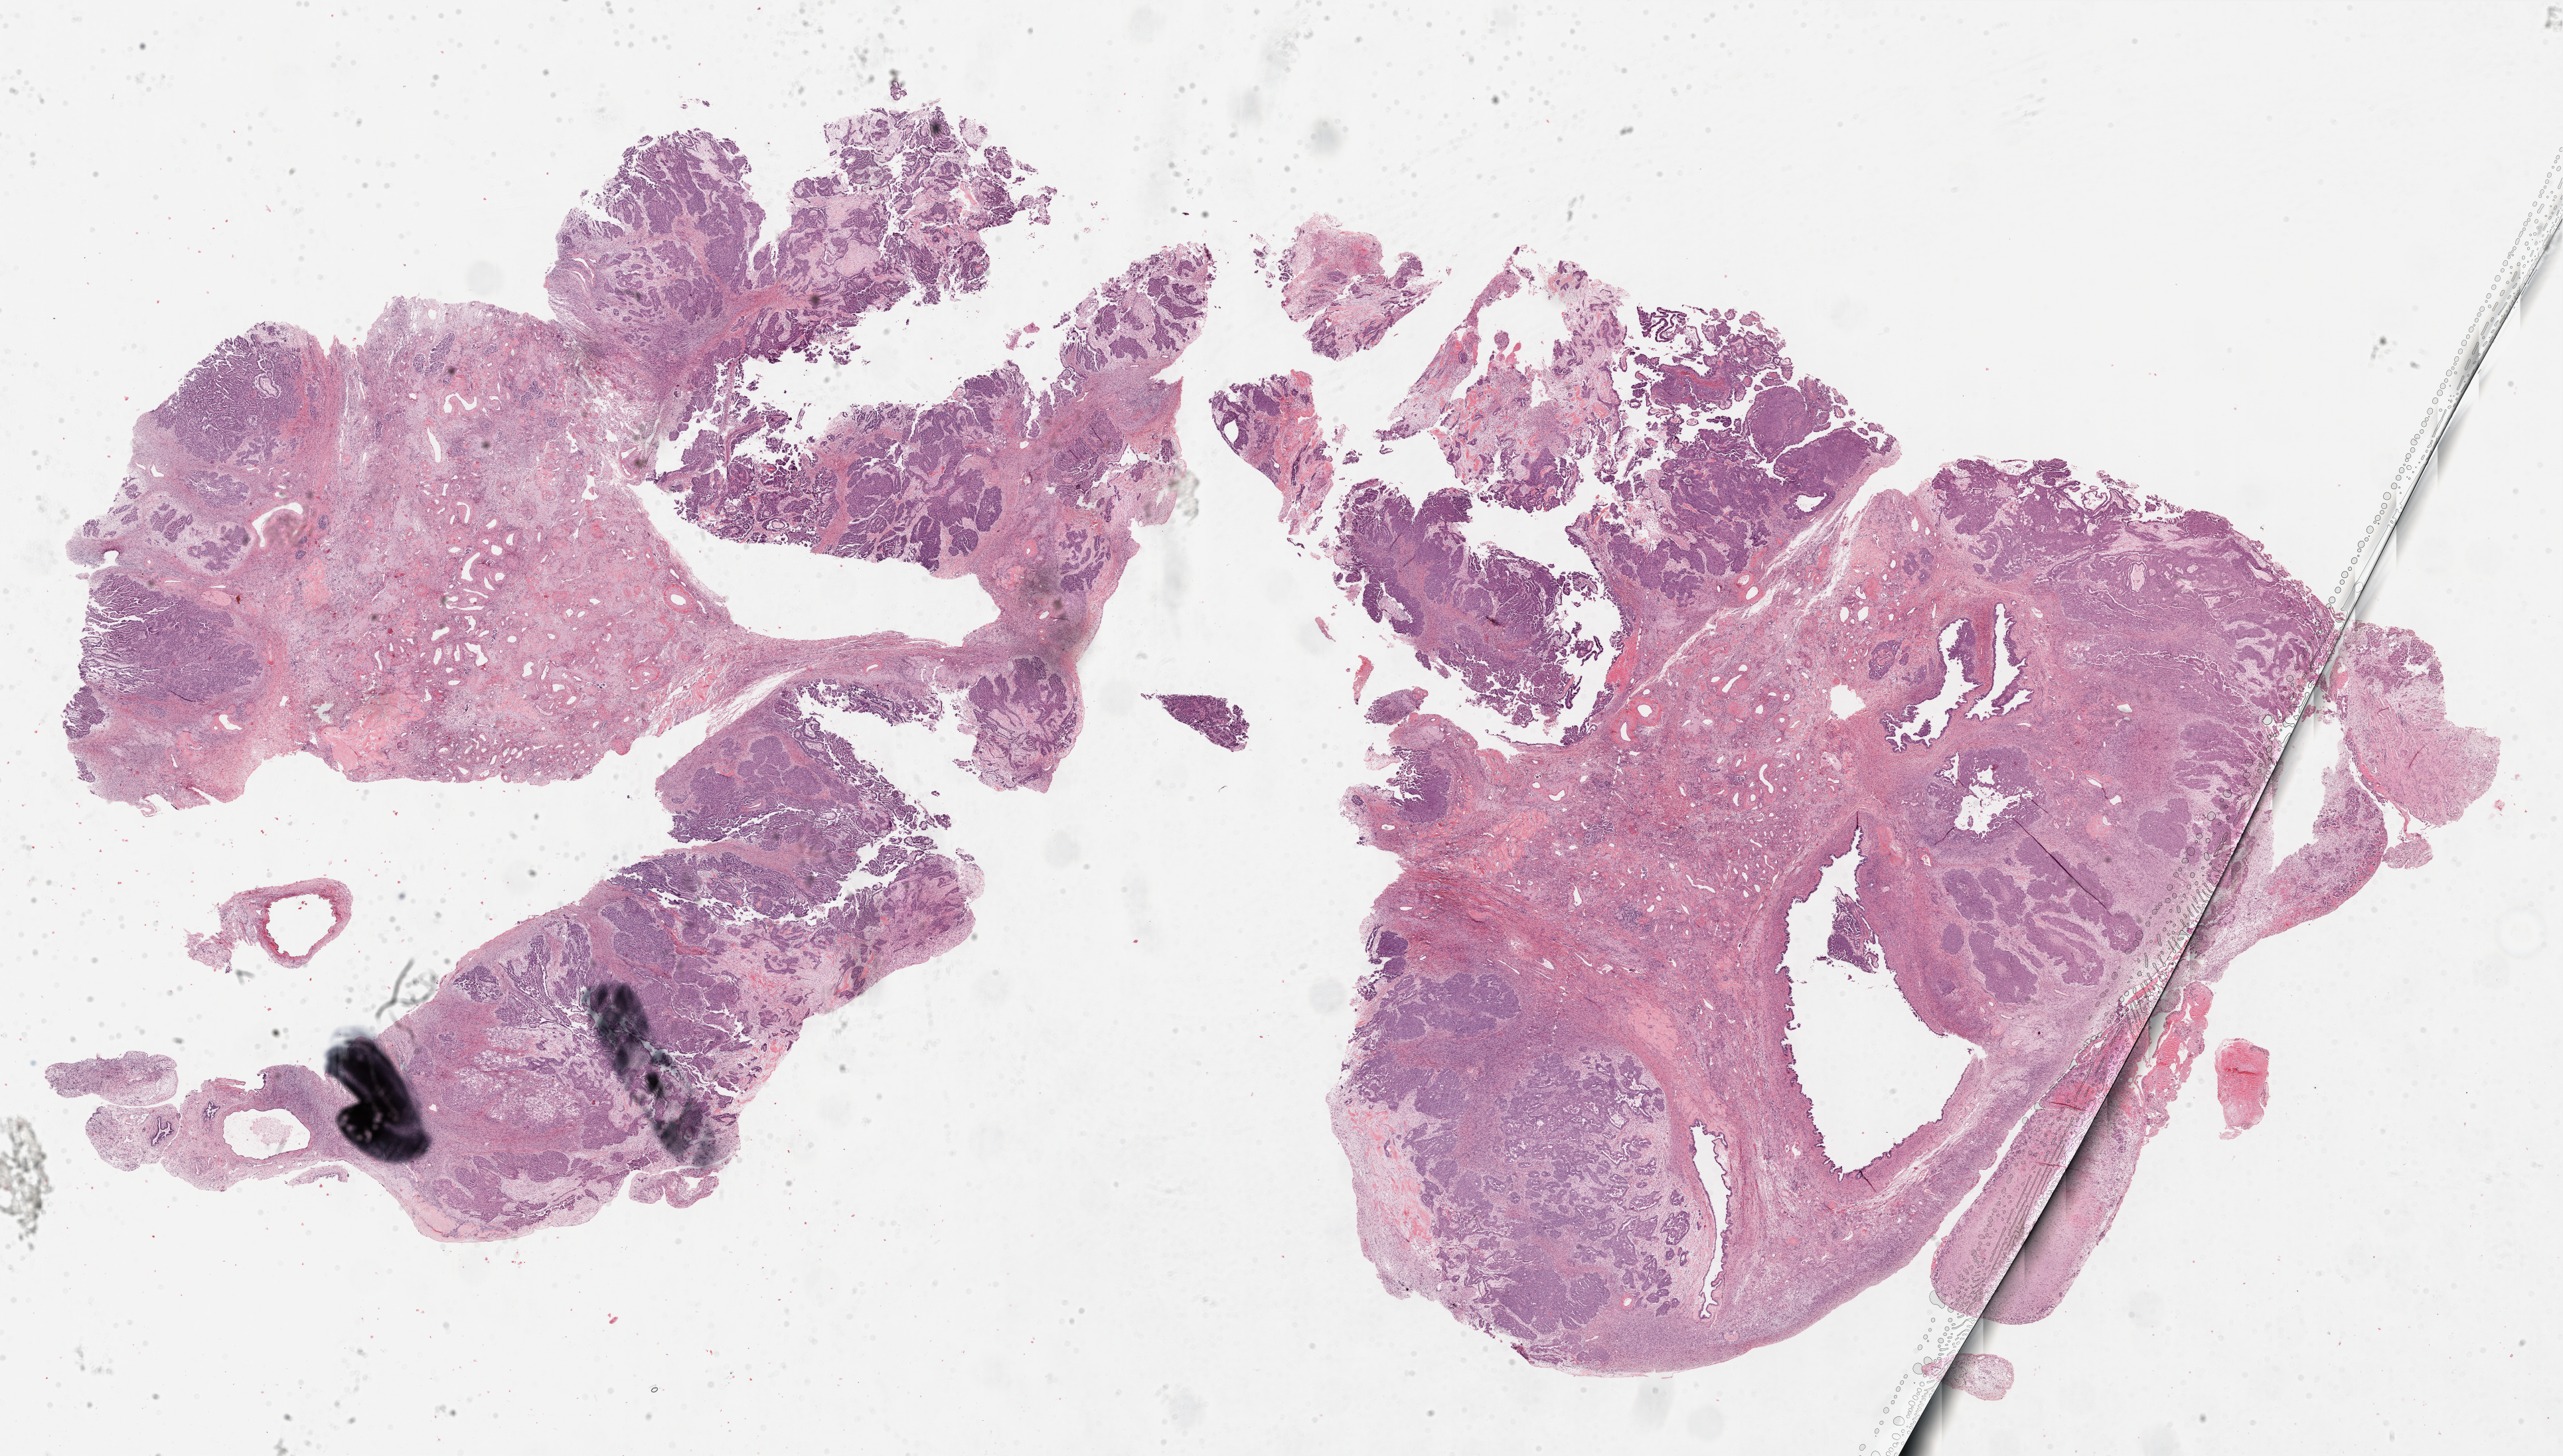
Digitized H&E-stained tissue section (whole slide) — whole scanned area (about 31.2 x 17.7 mm, from a 40x scan) shown as a low-resolution overview; FFPE section; ovary, primary tumour sample. Female patient; age at initial diagnosis 65 years. Histologic grade: G3 (poorly differentiated).
* laterality: right
* pathologic diagnosis: Serous cystadenocarcinoma, NOS
* FIGO stage: IIIC